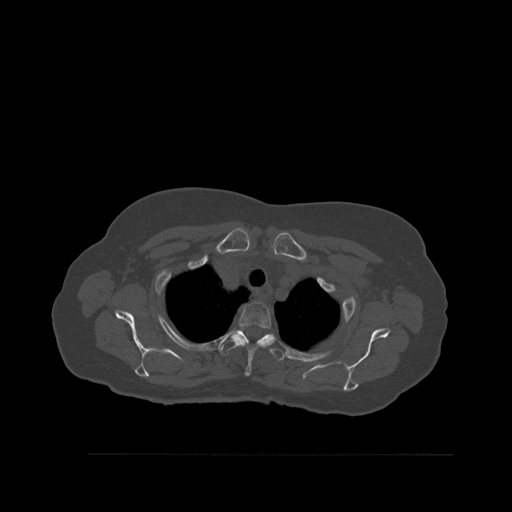
CT including the spine, one axial slice; position 427 of 527 along the scan axis; bone window (W 1800 / L 400 HU); 1.5 mm slice thickness; 512 × 512 image matrix, field of view 470 × 470 mm. Patient: female, 73 years. Case-level facts recorded for this patient, not image findings: primary cancer: breast.
Annotated regions visible in this slice (semi-automatically segmented with operator editing):
- T2 vertebra: bounding box <230,302,273,377> (left, top, right, bottom; pixels)
- T3 vertebra: <219,328,287,362>